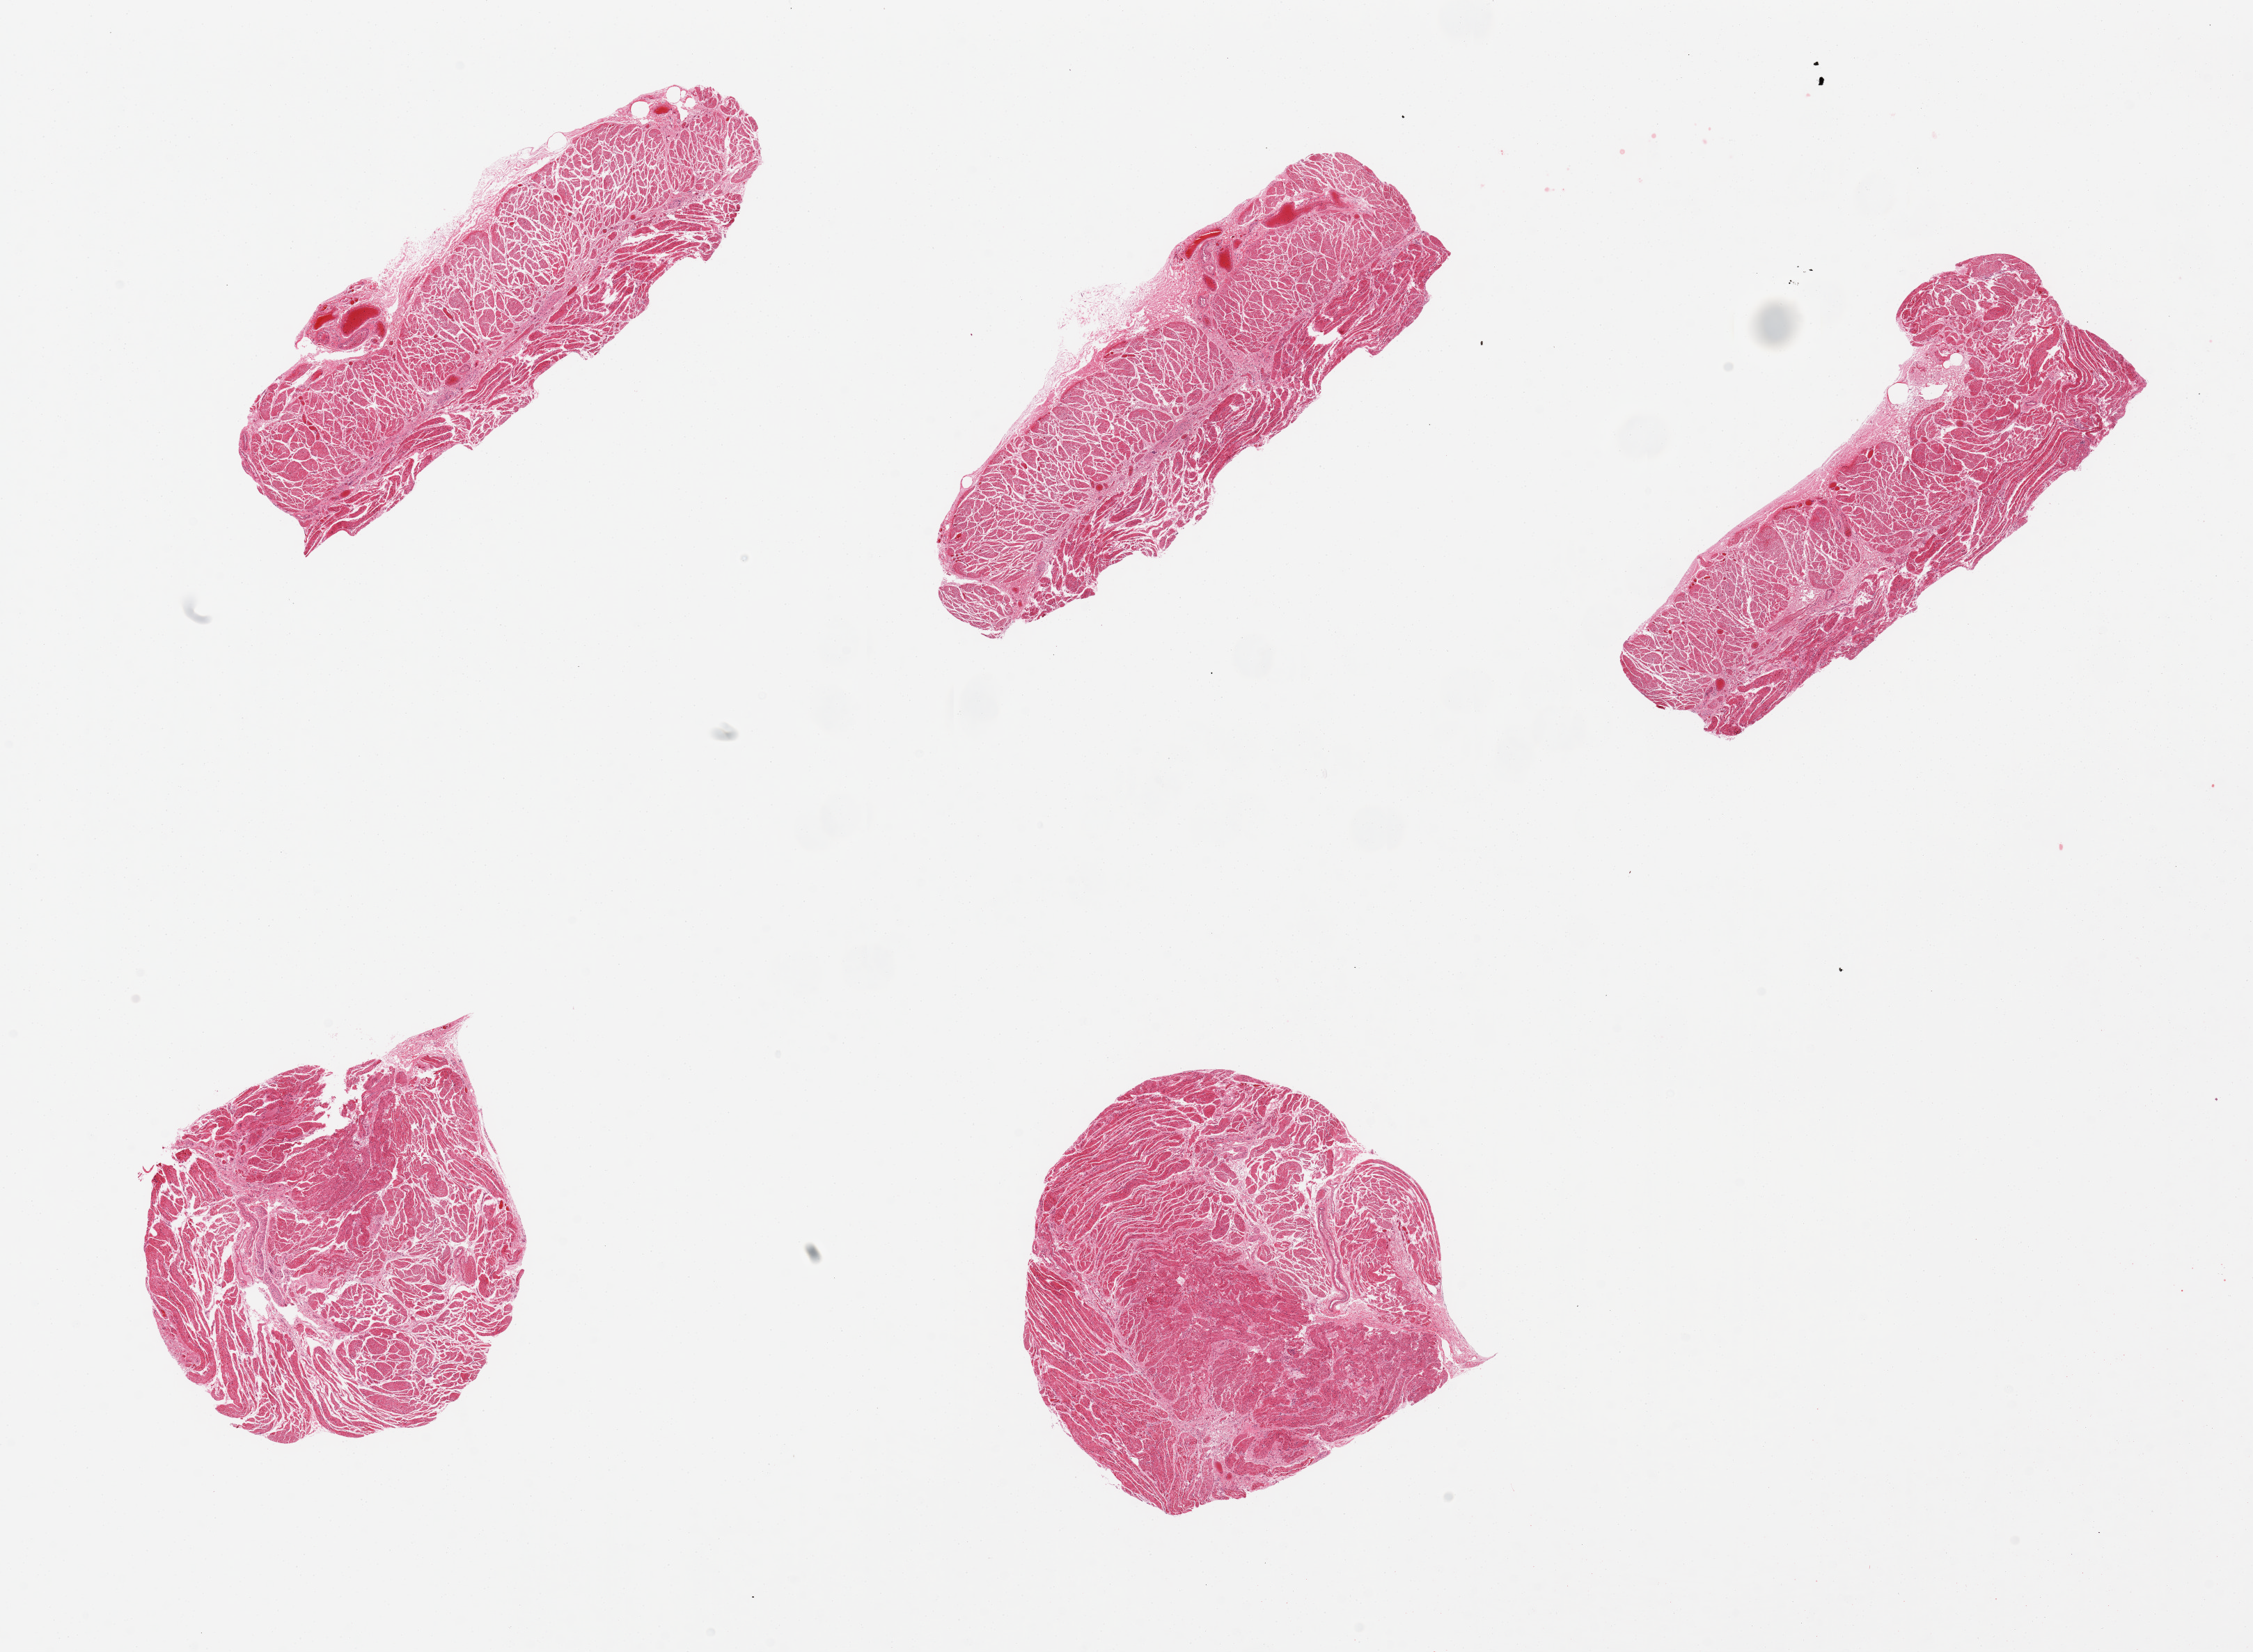
Digitized H&E-stained section — shown as a low-resolution overview of the whole scanned area (about 25.6 x 18.8 mm, slide scanned at 20x), PAXgene-fixed paraffin-embedded (PFPE) section, target tissue: gastroesophageal junction, tissue donor sample. Female donor.
Review note (as recorded): 5 pieces, all muscularis.